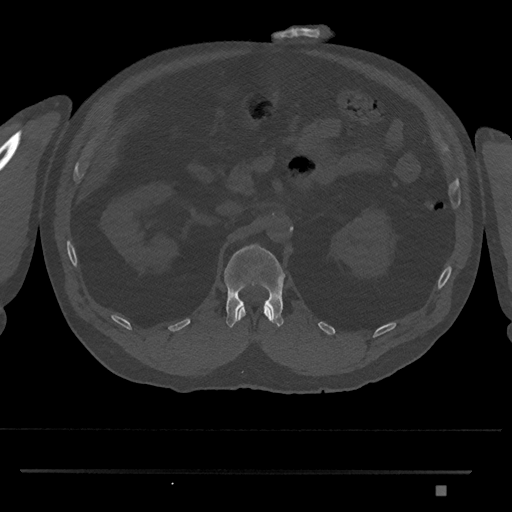
CT including the spine, one axial slice. Slice 842 of 1134 in the series (ordered by position). 120 kVp. Bone window (W 1800 / L 400 HU). 0.5 mm slice thickness. 512 × 512 image matrix, field of view 429 × 429 mm. Male patient, age 65 years. From the clinical record (not read from this slice): primary cancer: prostate.
Structures marked on this image (semi-automatically segmented with operator editing):
- L1 vertebra: bounding box [x1, y1, x2, y2] px = [224, 244, 285, 328]
- T12 vertebra: [237, 306, 272, 322]